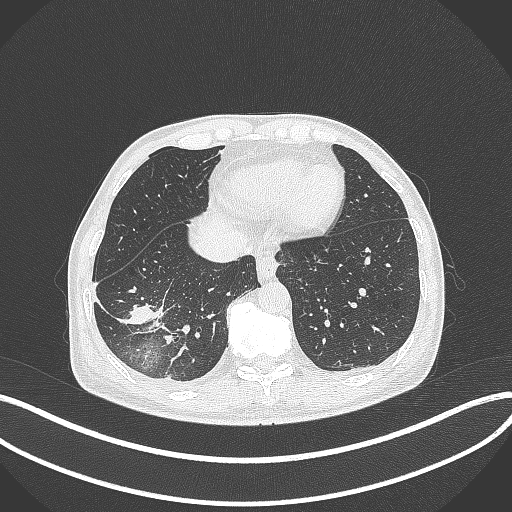
Chest CT, one axial slice; slice 98 of 388 in the series (ordered by position); 120 kVp; lung window (W 1500 / L -600 HU); 512 × 512 image matrix, field of view 400 × 400 mm. Male patient, age 64 years. Case-level facts recorded for this patient, not image findings: clinical TNM (as recorded): T3 N0 M0; histopathological grade: G2-3.
Structures marked on this image (rectangle marked by the reading radiologist):
- lung tumour (recorded histology: adenocarcinoma): bounding box [x1, y1, x2, y2] px = [113, 298, 175, 328]